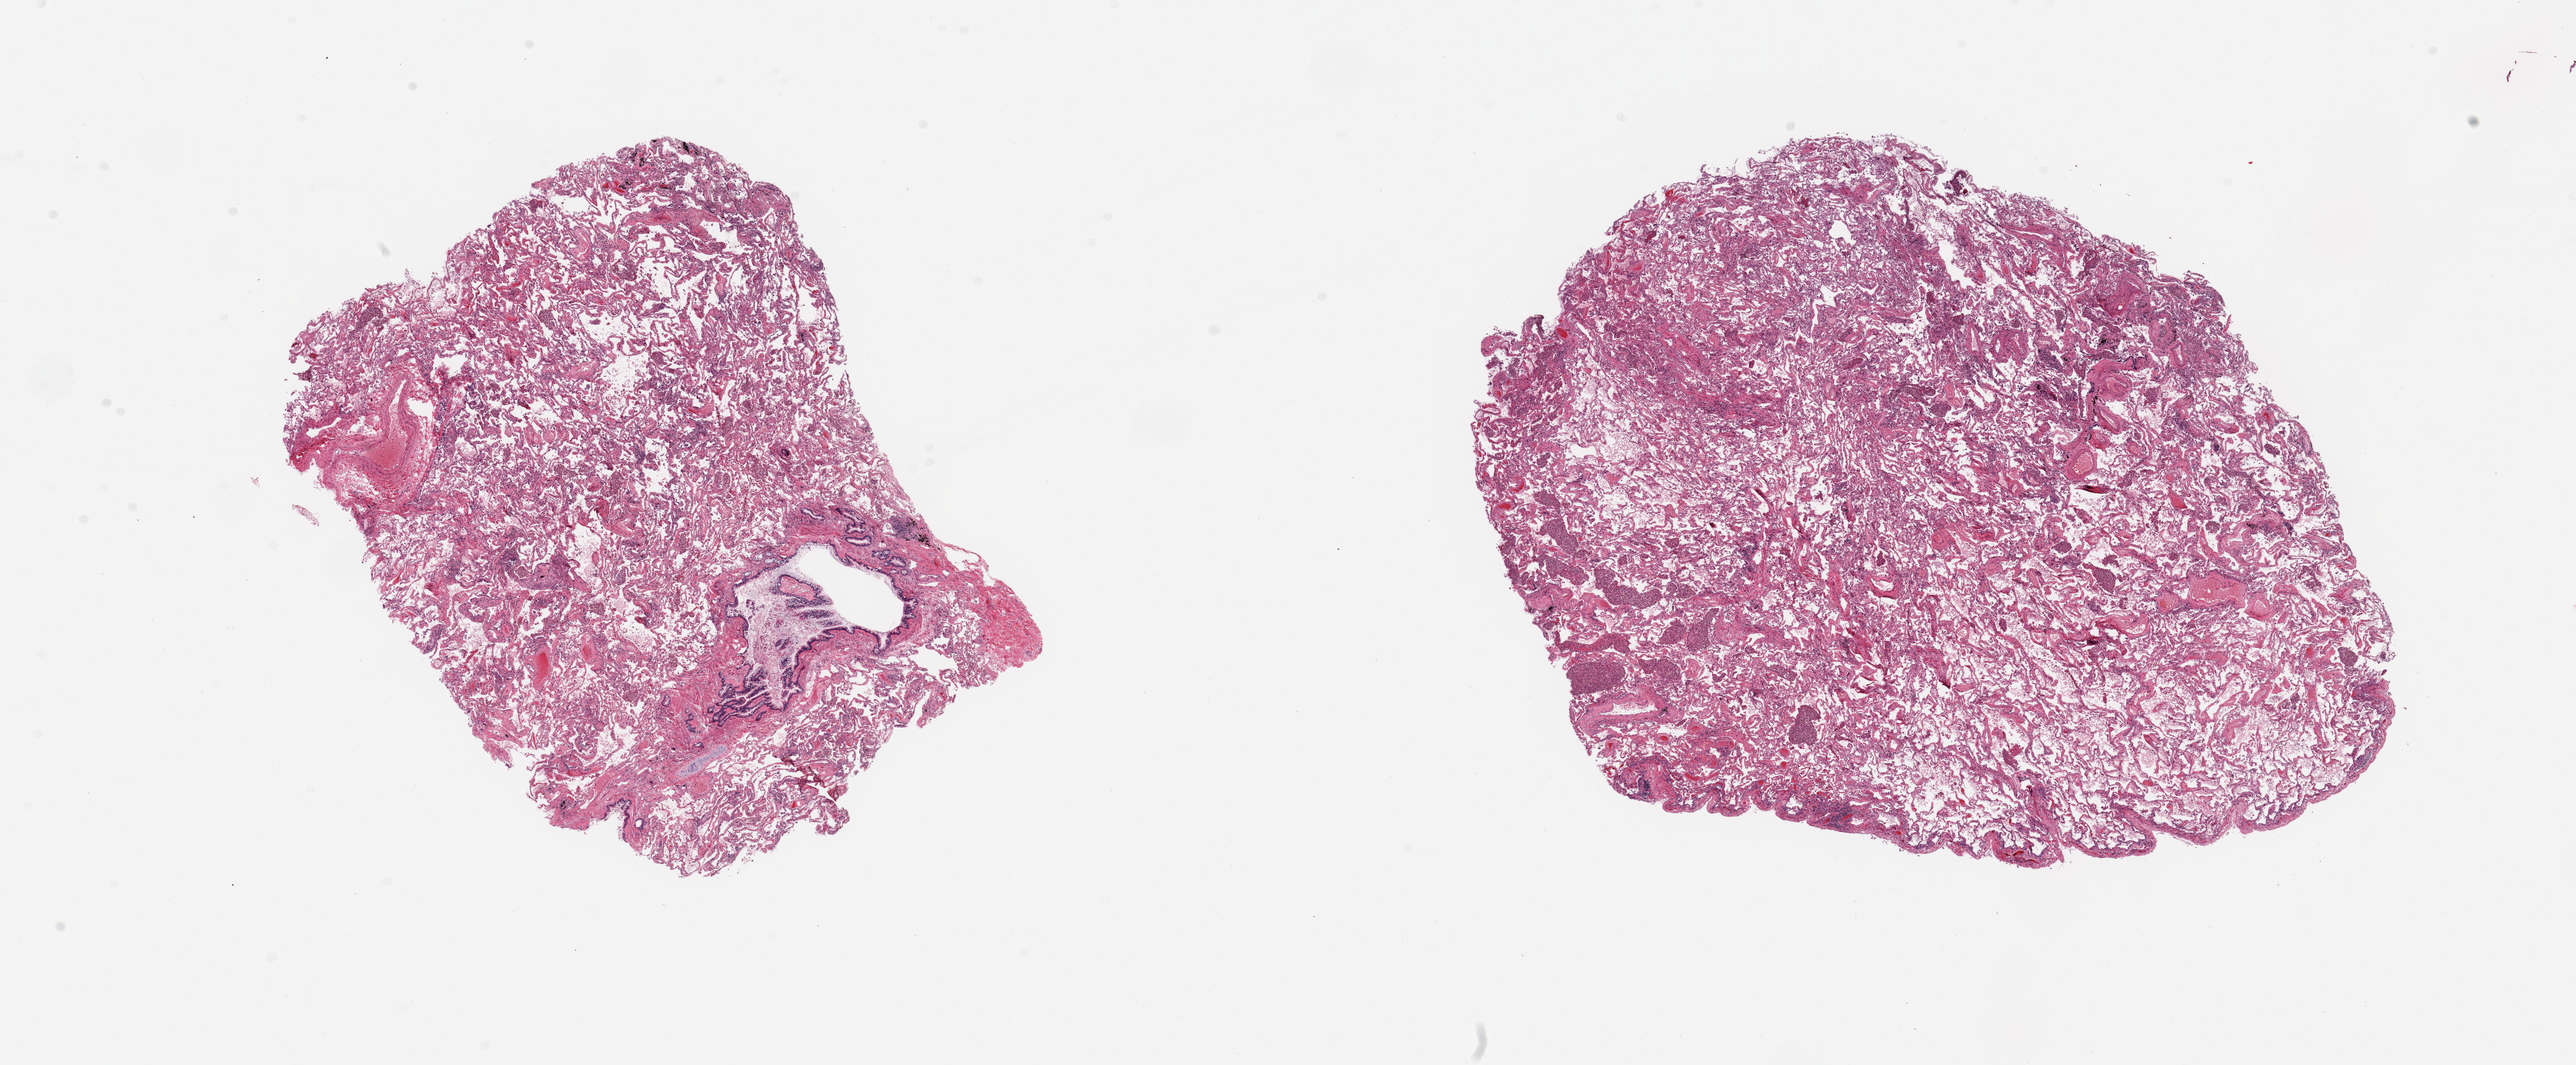
Digitized hematoxylin and eosin (H&E)-stained section, brightfield — whole scanned area (about 26.6 x 11.0 mm) shown as a low-resolution overview. PAXgene-fixed paraffin-embedded (PFPE) section. Target tissue: lung. Tissue donor sample. Donor: male.
Pathologist's review note for this sample: 2 pieces diffuse chronic congestion/edema, moderate-marked.